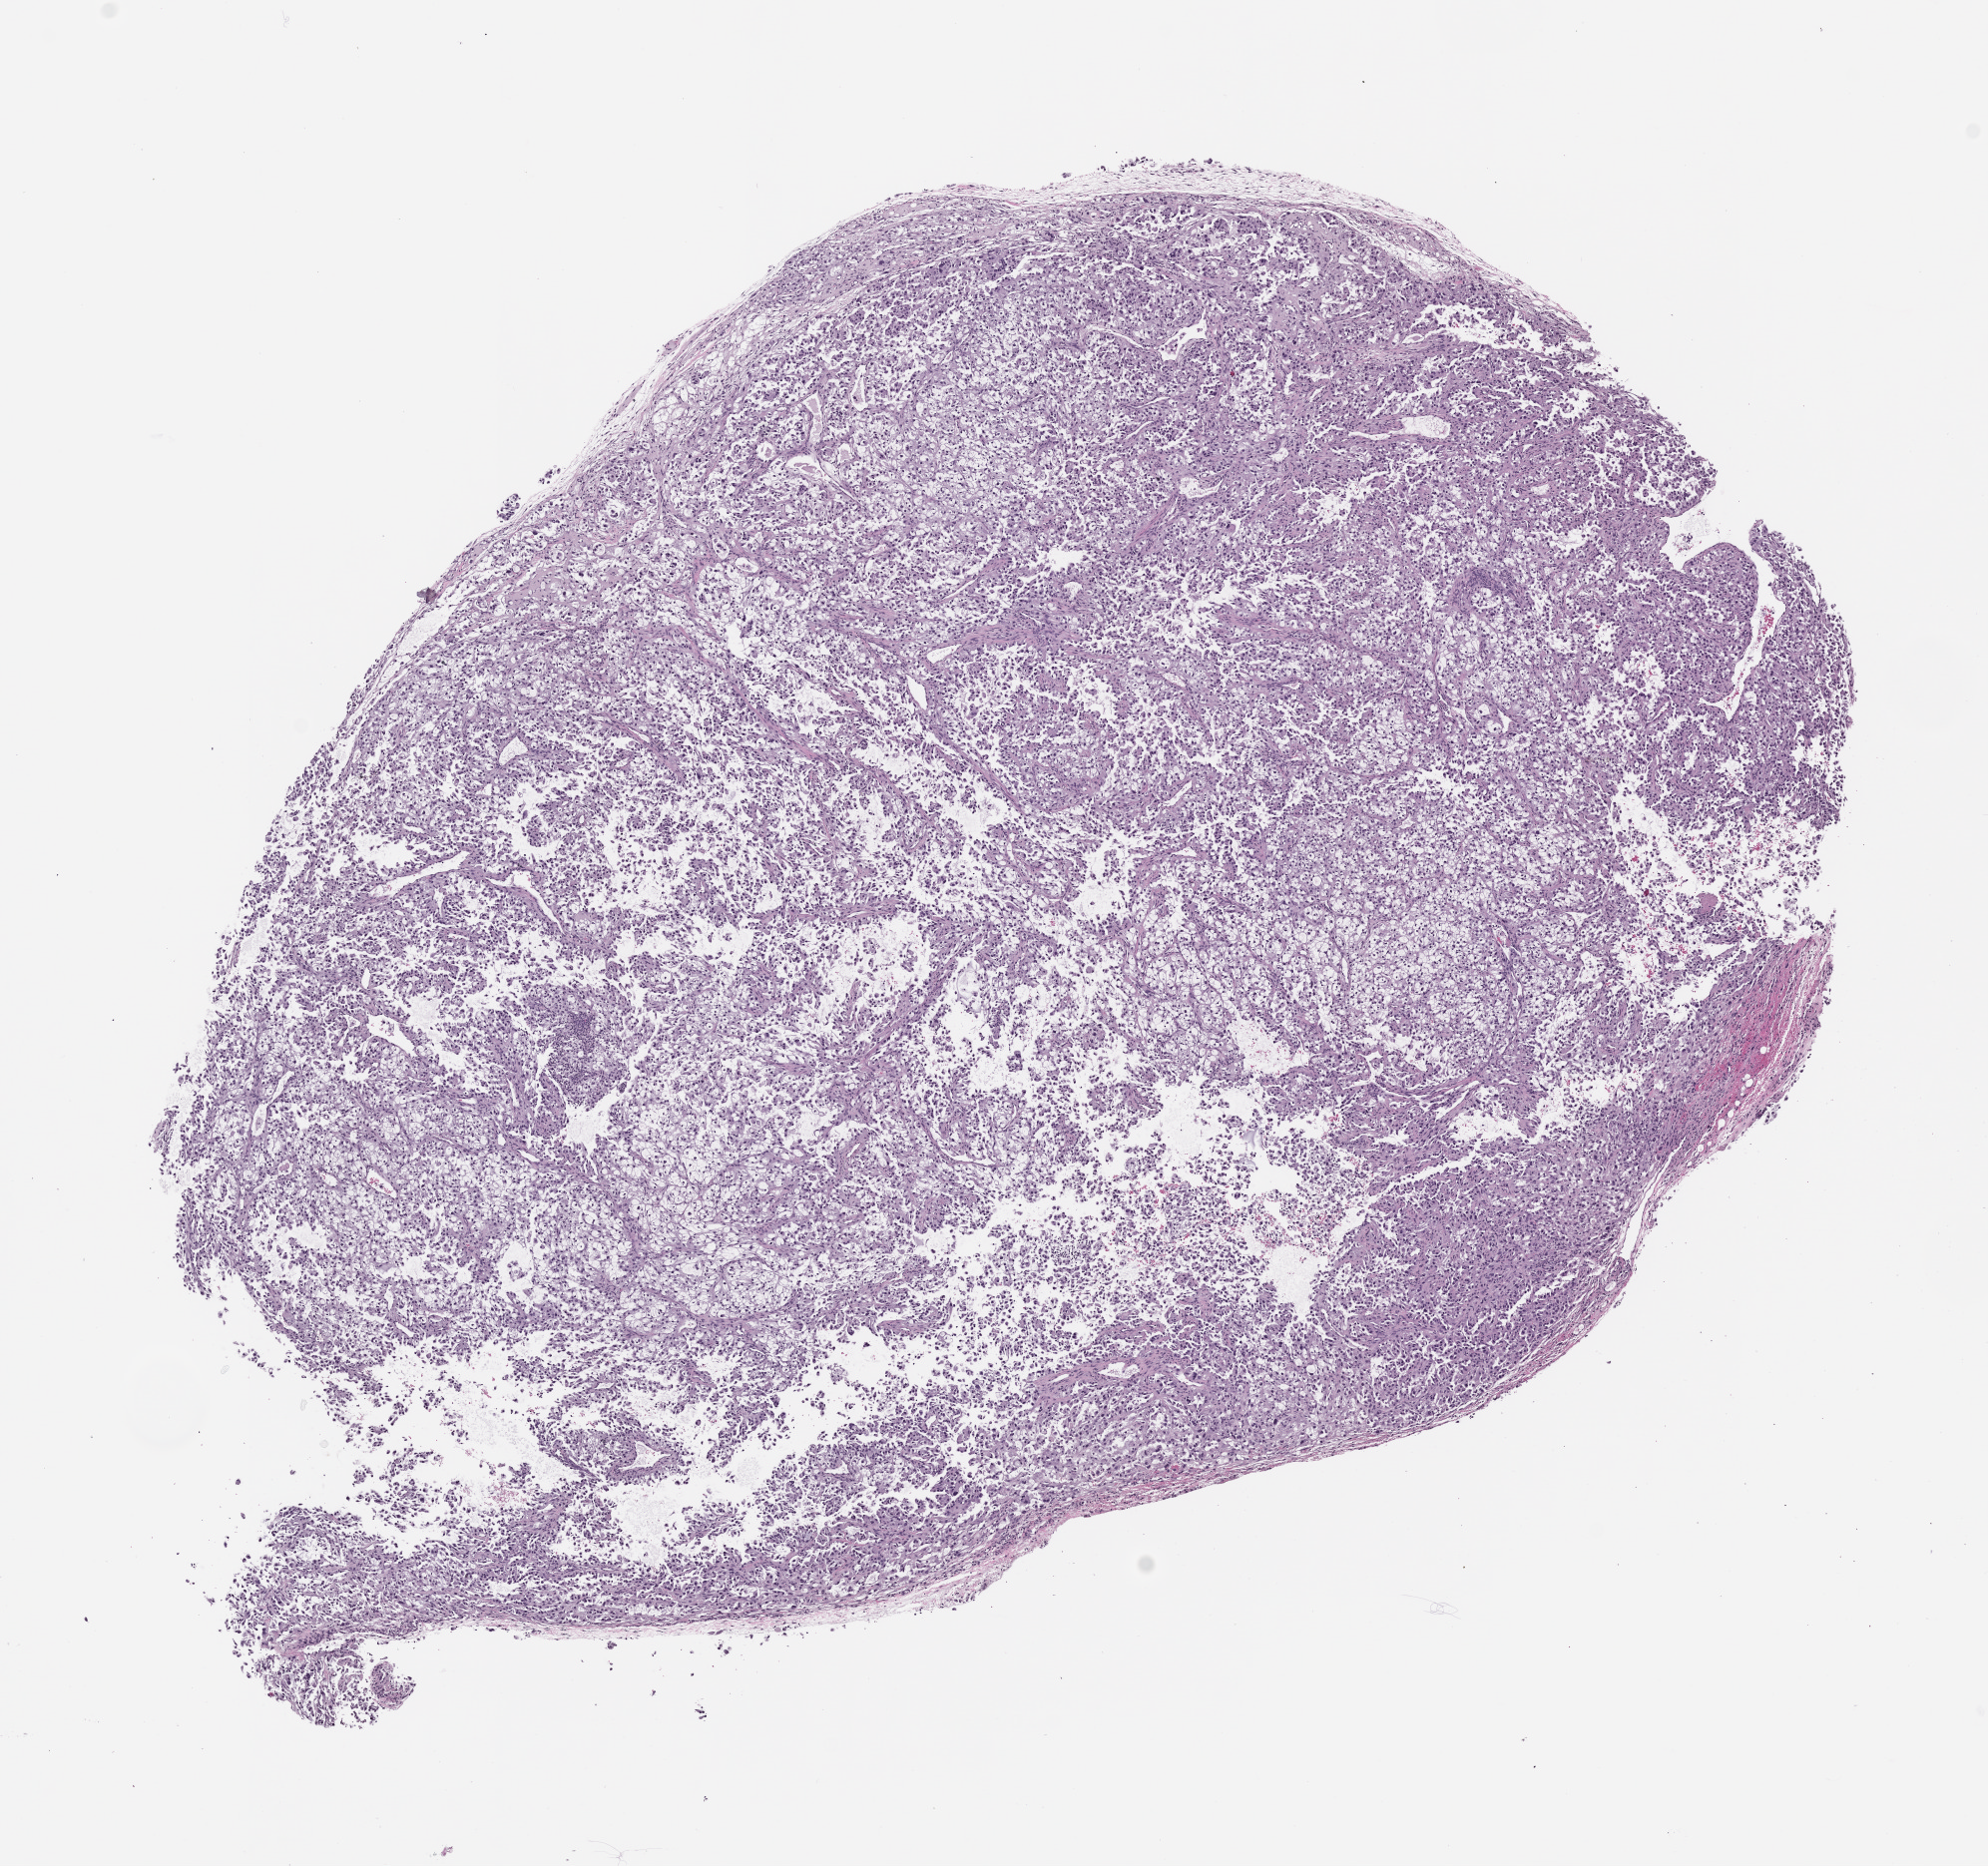
Whole-slide image, hematoxylin and eosin (H&E): patient-derived xenograft (human tumor grown in a mouse), passage 1, shown as a low-resolution overview of the whole scanned area (about 8.0 x 7.5 mm), formalin-fixed, paraffin-embedded (FFPE) tissue, tumor site category: genitourinary tract.
Originating patient diagnosis: Renal Cell Carcinoma, Not Otherwise Specified.